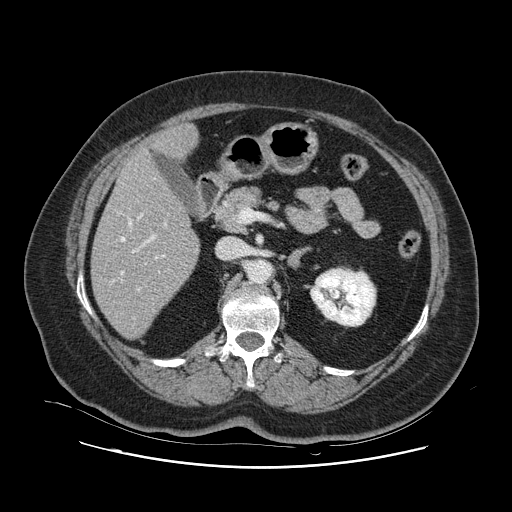
Contrast-enhanced abdominal CT, one axial slice; slice 50 of 132 in the series (ordered by position); 120 kVp; soft-tissue window (W 400 / L 40 HU); 2.5 mm slice thickness; 512 × 512 image matrix, field of view 391 × 391 mm. Female patient, age 73 years. Case-level facts recorded for this patient, not image findings: diagnosis: colorectal cancer liver metastases, imaged before liver resection; multiple liver metastases: no.
Structures marked on this image (outlined manually by an expert reader):
- hepatic veins: bounding box <111,178,166,319> (left, top, right, bottom; pixels)
- liver: <92,126,200,338>
- planned liver remnant (the part of the liver to remain after resection): <93,149,200,338>
- portal vein (with intrahepatic branches): <137,223,167,291>